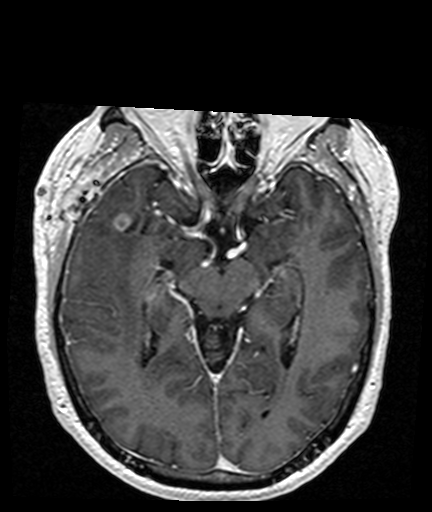
Brain MRI from a brain-tumour surgery series, one axial slice; position 100 of 176 along the scan axis; T1-weighted post-contrast; 1 mm slice thickness; 432 × 512 image matrix, field of view 194 × 230 mm. Case-level facts recorded for this patient, not image findings: histopathology: Glioblastoma; WHO grade: 4; IDH mutation: no; tumour location: Right Frontal Temporal, Posterior Sylvian Fissure.
Annotated regions visible in this slice (outlined manually by an expert reader):
- tumour: bounding box [x1, y1, x2, y2] px = [114, 214, 132, 231]